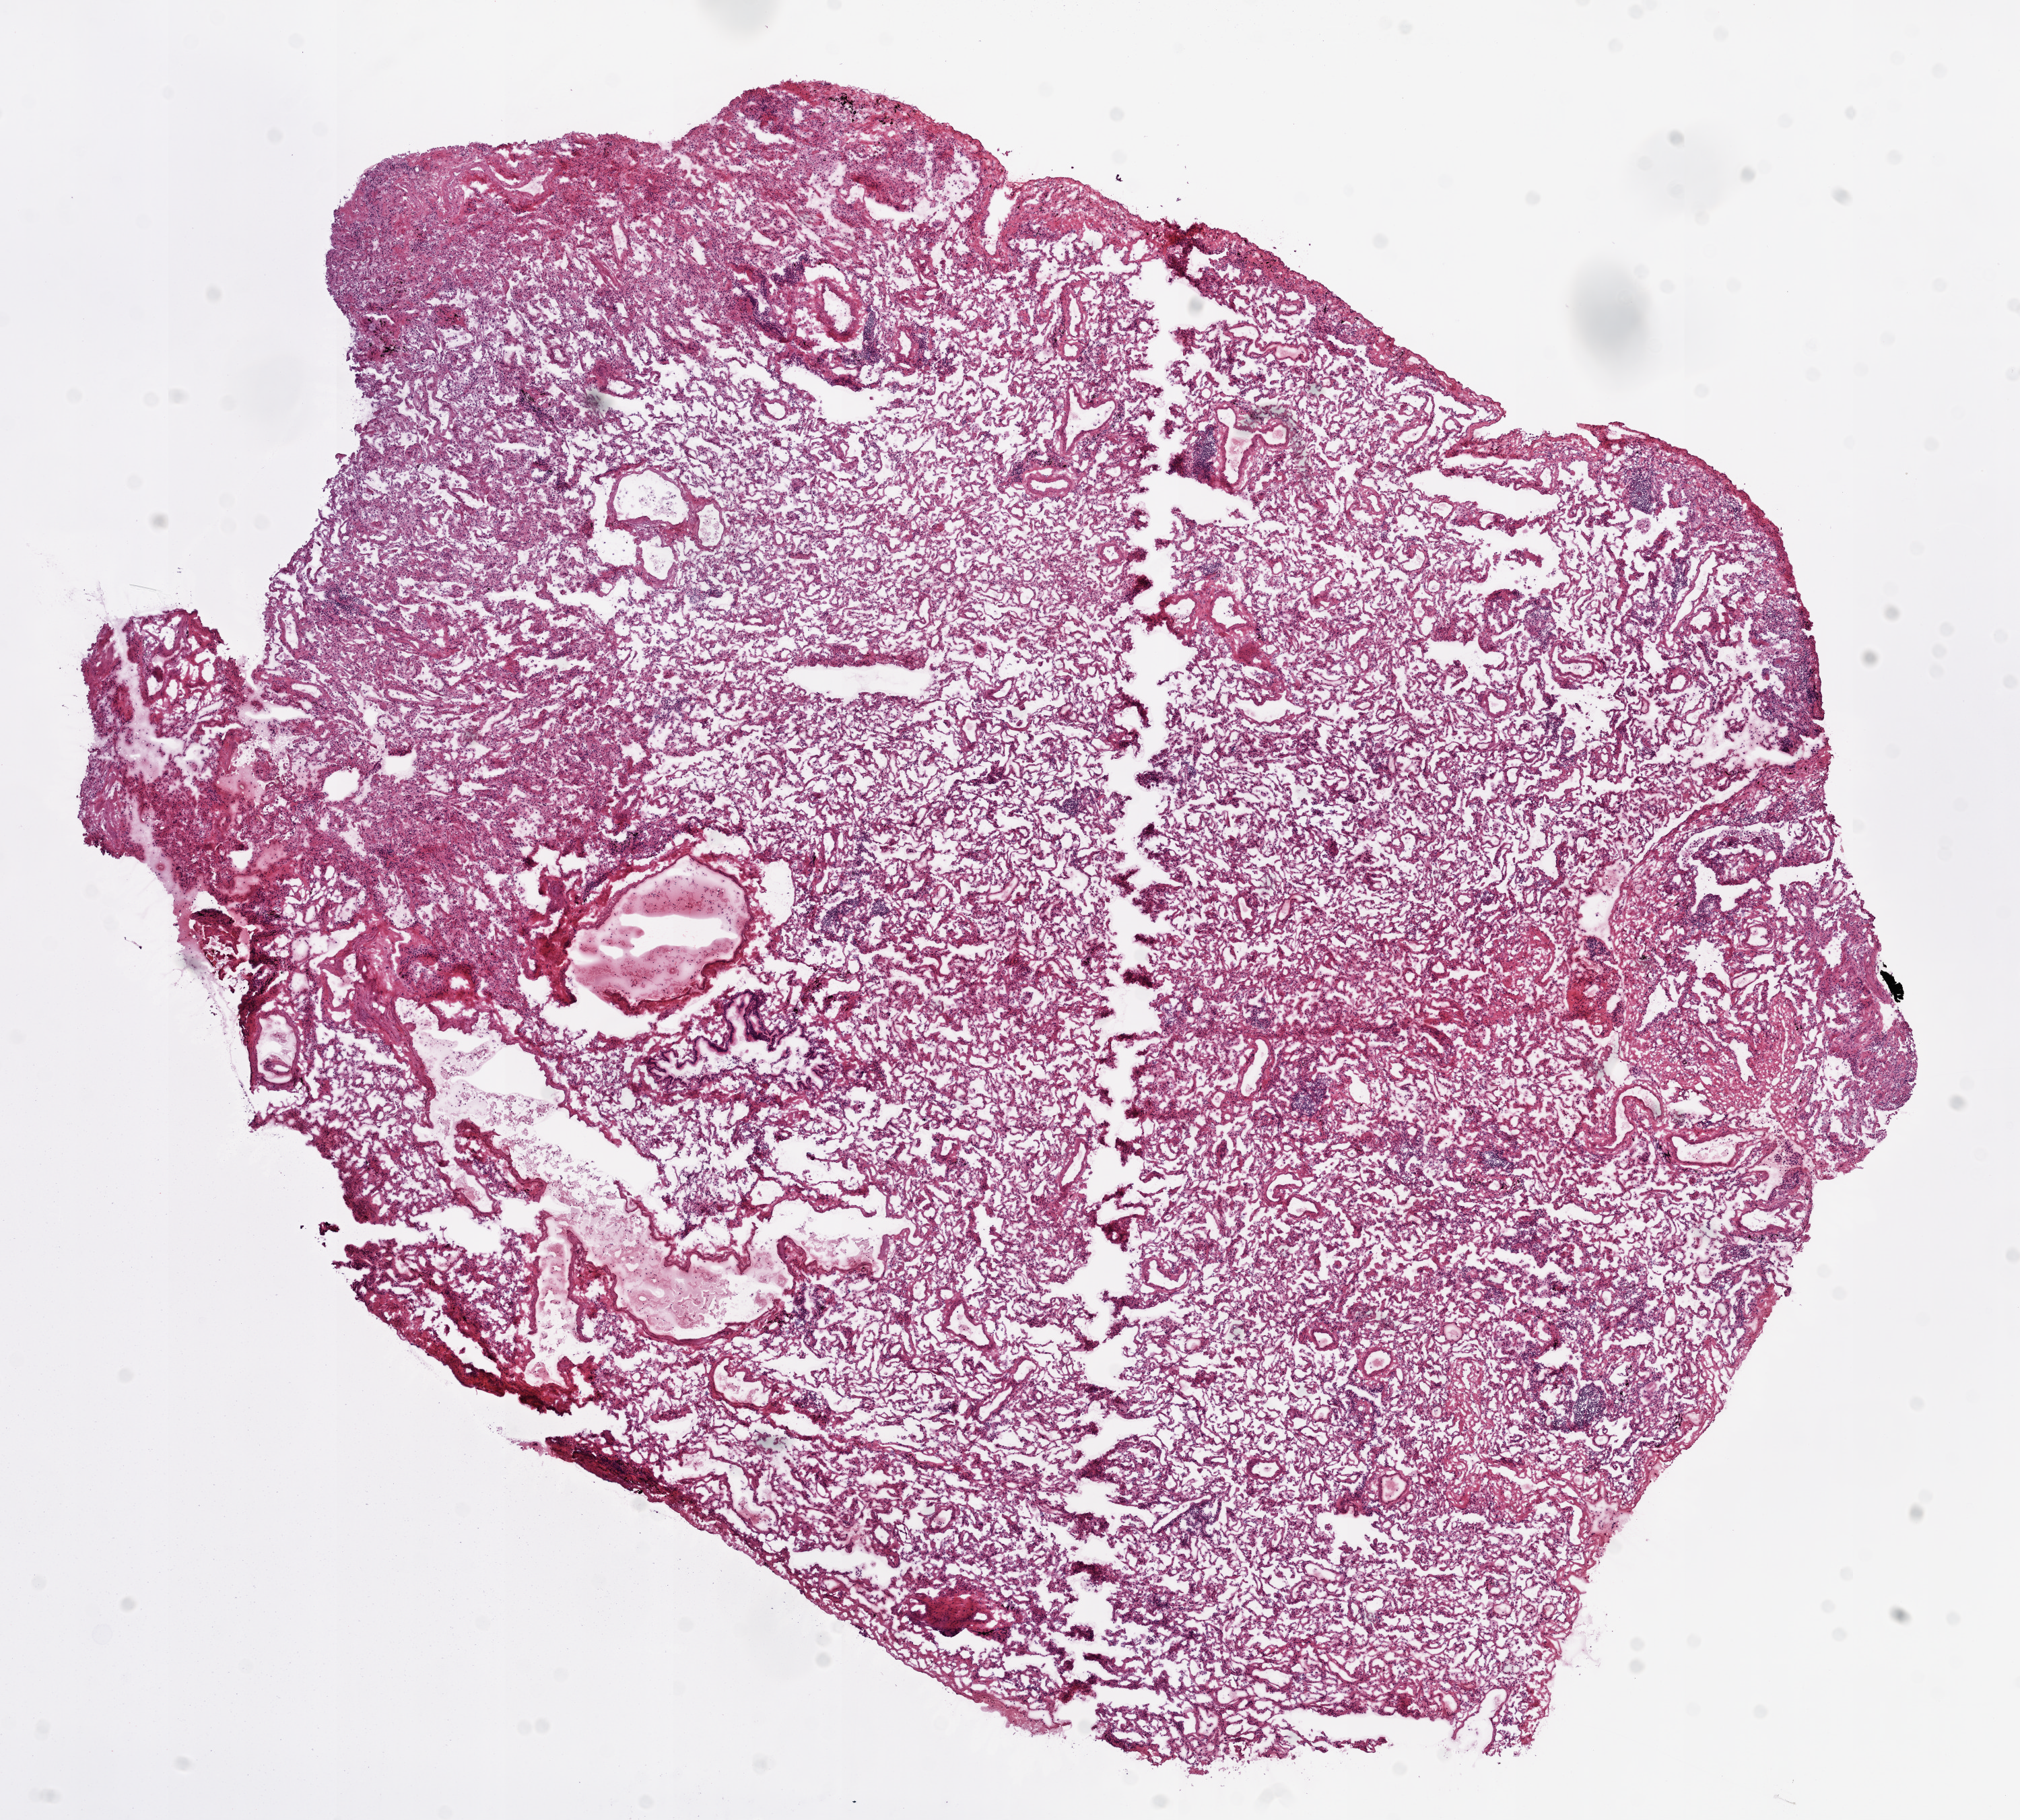
H&E-stained whole-slide image, low-resolution overview of the scanned area, about 12.0 x 10.8 mm (acquisition: 20x scan); frozen section from the top of the tissue portion; solid tissue normal (non-tumour tissue) sample from the lung. Female patient; age at initial diagnosis 74 years.
This section: solid tissue normal (non-tumour) sample from the same patient. Patient diagnosis: Adenocarcinoma, NOS (lower lobe, lung).